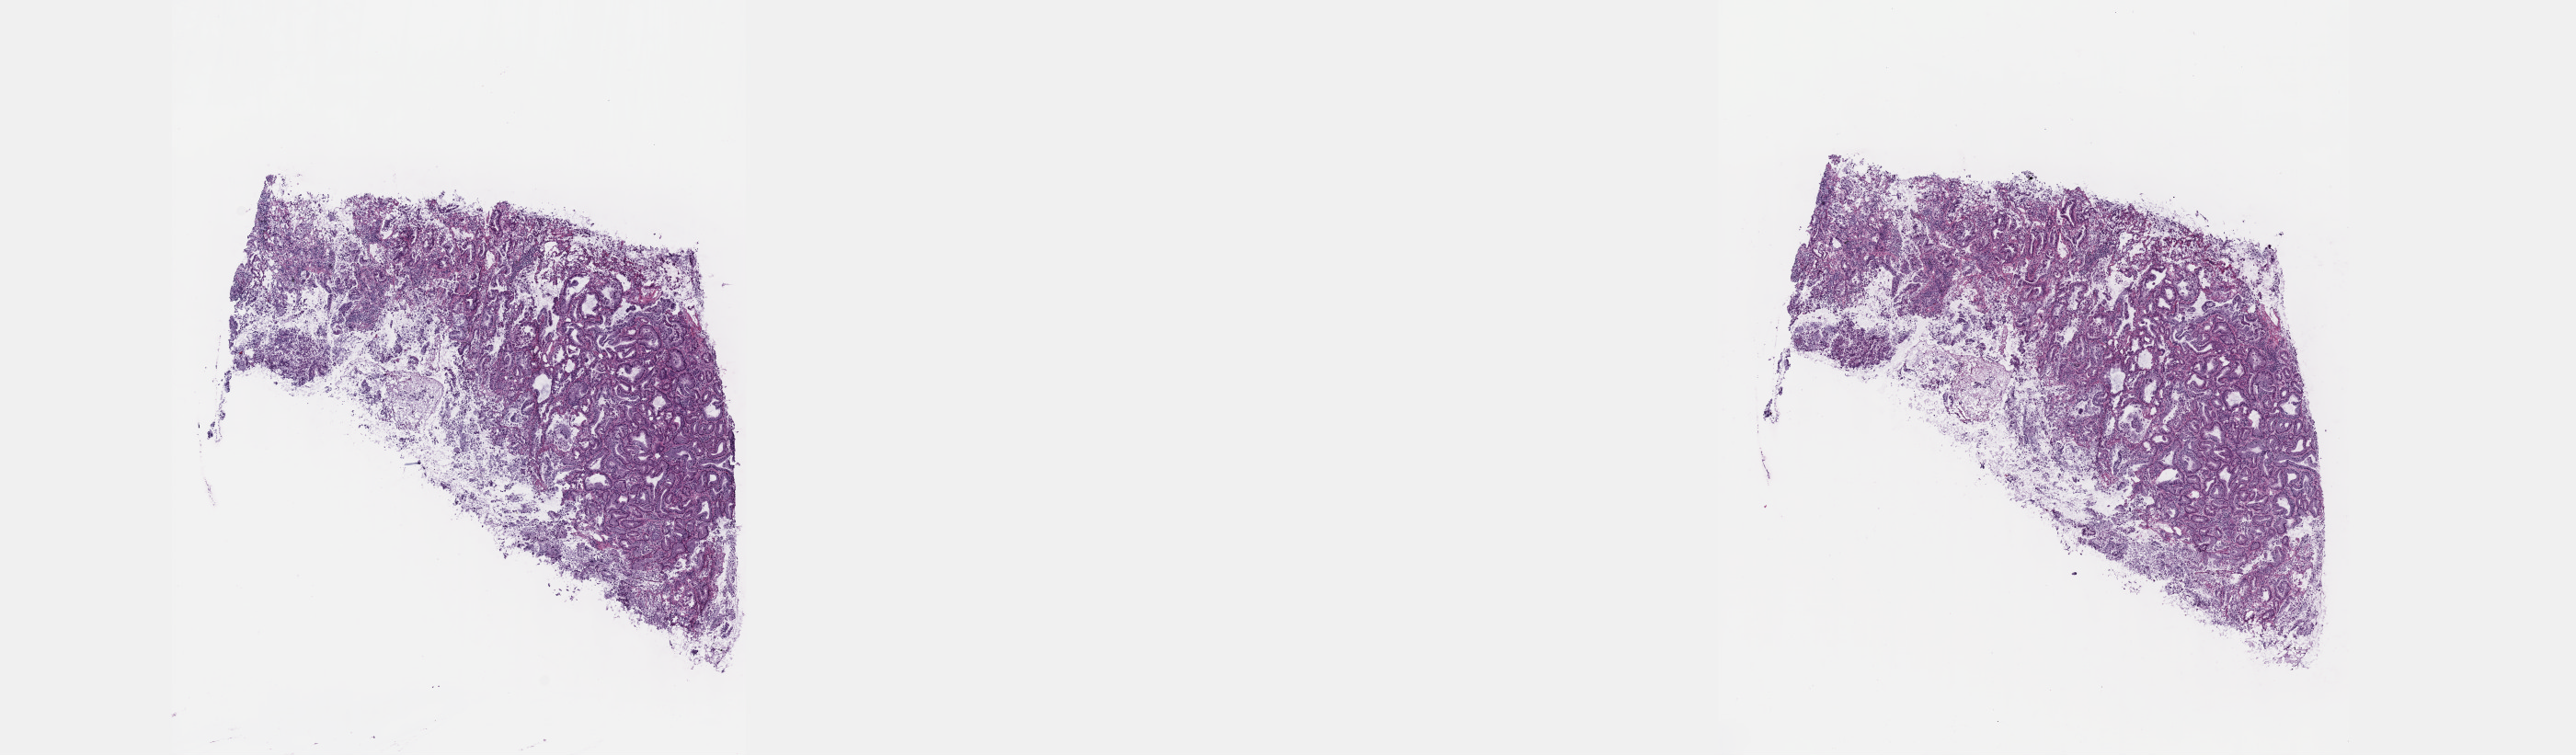
Digitized H&E tissue section (whole slide), shown as a low-resolution overview of the whole scanned area (about 22.6 x 6.6 mm, acquisition: 40x scan), frozen section from the top of the tissue portion, primary tumour sample from the lung. Female, age 68 years at initial diagnosis. Slide review estimates, as recorded: tumour cells 100%, tumour nuclei 60%, normal cells 0%, stromal cells 0%, necrosis 0%. Inflammatory infiltration, as recorded: lymphocyte infiltration 0%, monocyte infiltration 0%, neutrophil infiltration 0%.
* histologic diagnosis: Bronchio-alveolar carcinoma, mucinous (upper lobe, lung)
* TNM: T1b N0 M0
* AJCC pathologic stage: IA